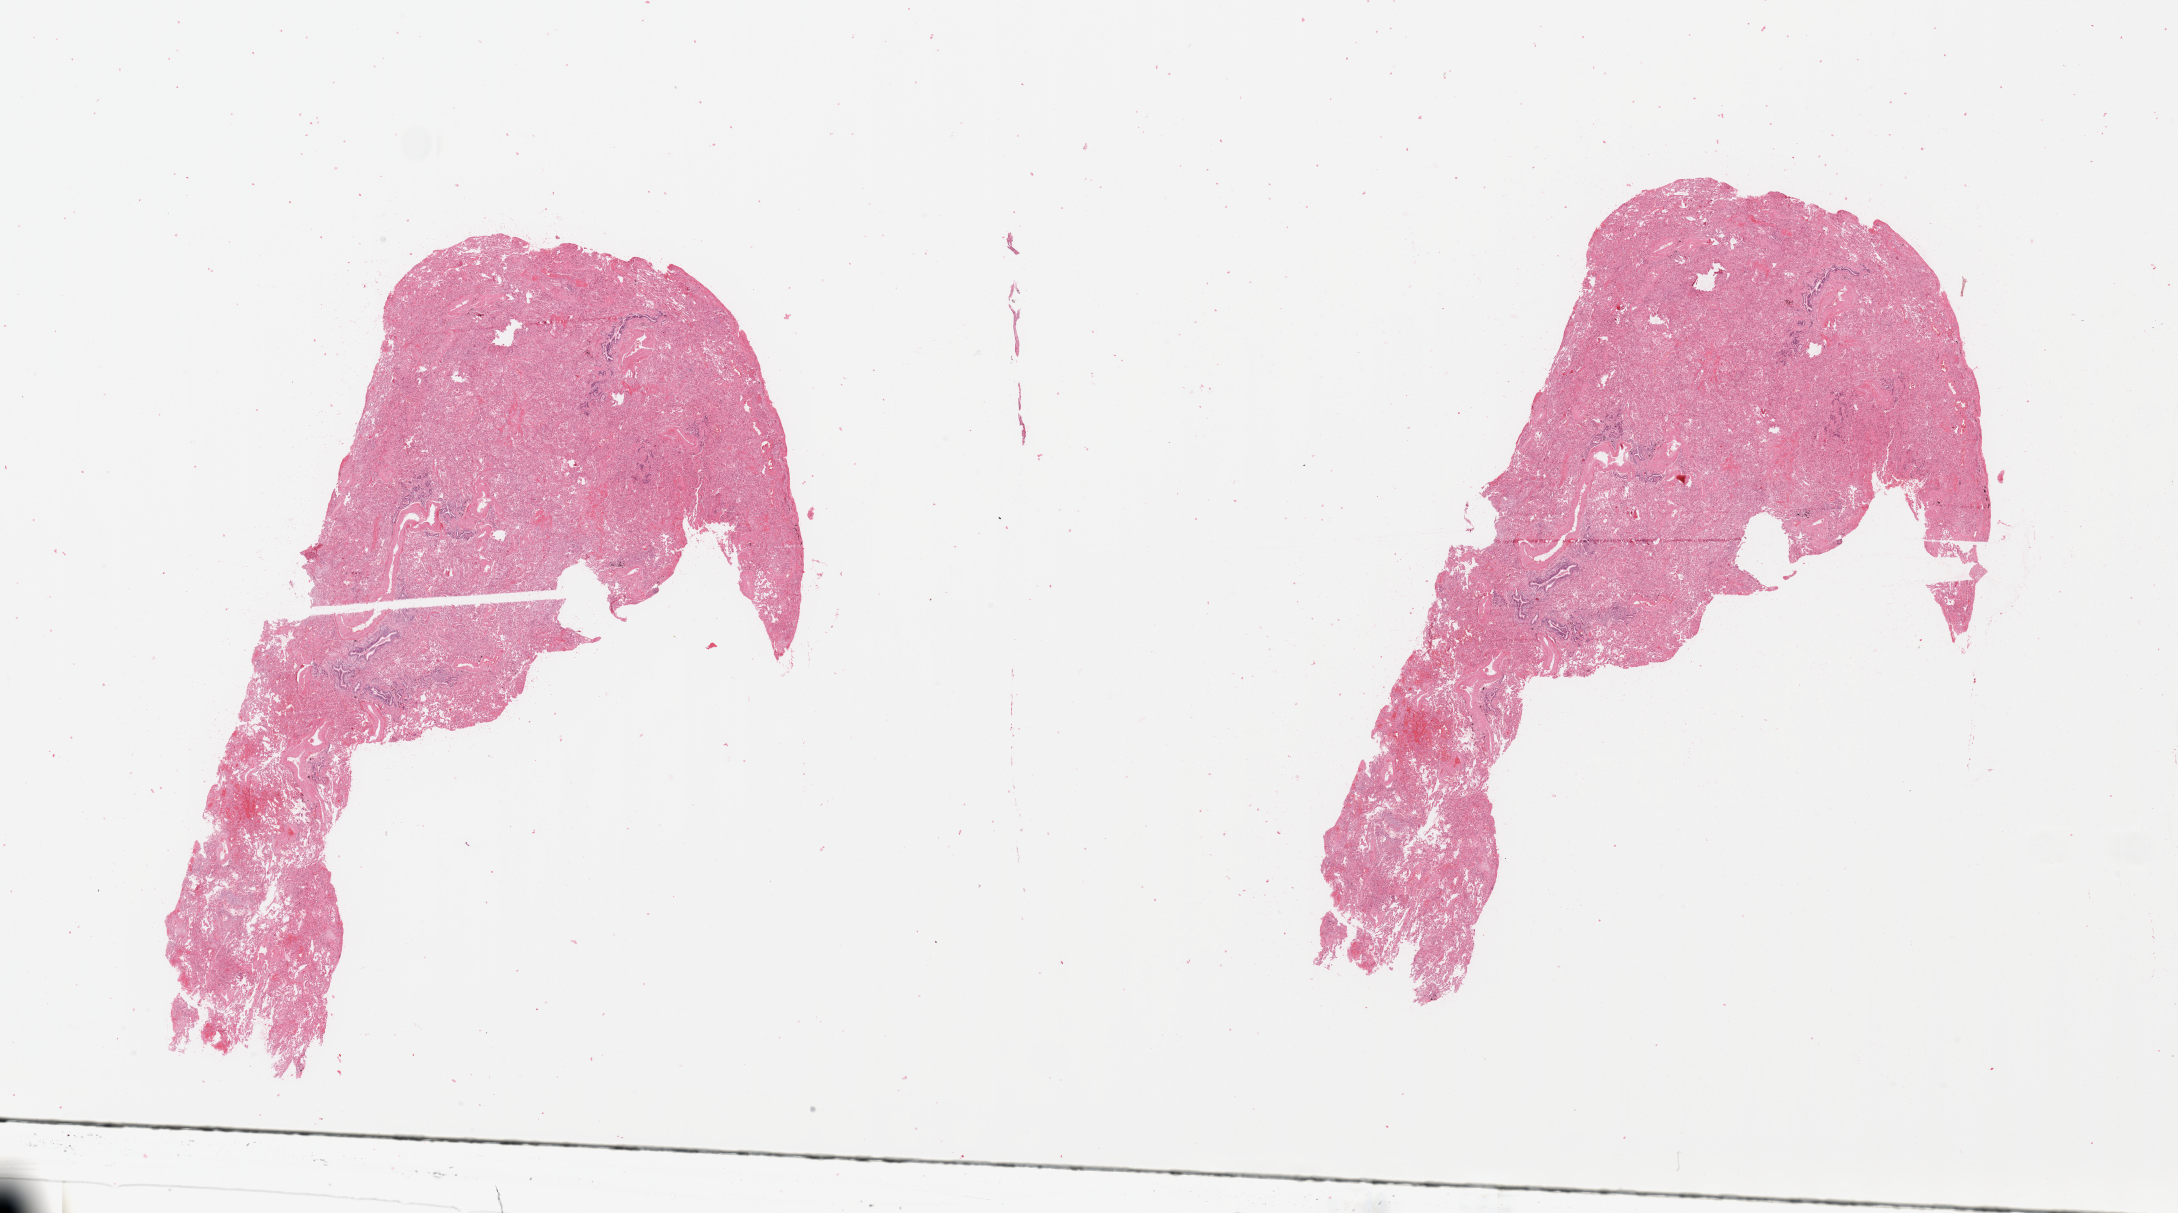
Whole-slide histology image, H&E-stained — a low-resolution overview of the entire scanned area, about 34.5 x 19.2 mm; normal (non-tumour) tissue sample, lung. 67-year-old male patient.
This section: normal (non-tumour) tissue from the same patient. Patient diagnosis: Adenocarcinoma, NOS.